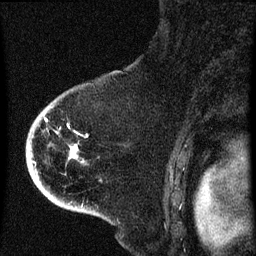
Breast MRI (dynamic contrast-enhanced), one sagittal slice. Dynamic contrast-enhanced series, image 2 of 4 at this slice position (ordered by acquisition). 1.5 T. TE 4.2 ms, TR 8 ms. 2 mm slice thickness. 256 × 256 image matrix. Female patient, age 71 years.
Annotated regions visible in this slice (semi-automatic segmentation, software-assisted and operator-edited):
- analysis volume of interest (the breast-tissue region the enhancement analysis was run in; not a lesion): bounding box <32,86,103,205> (left, top, right, bottom; pixels)
- tumour enhancement mask (voxels above the 70 % enhancement threshold inside the analysis volume of interest): <35,118,76,165>